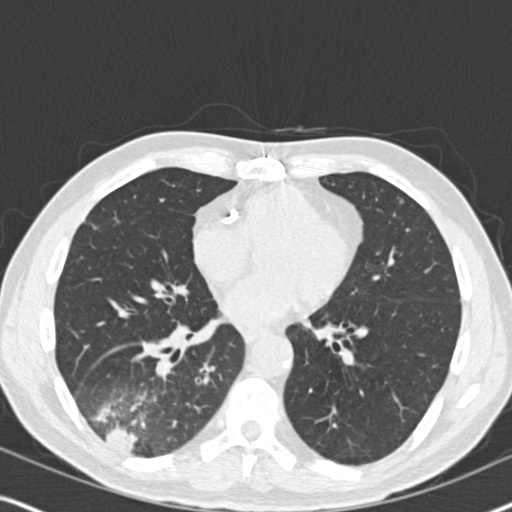
Low-dose screening chest CT, one axial slice; position 85 of 182 along the scan axis; reconstruction kernel B30f; lung window (W 1500 / L -600 HU); 2 mm slice thickness; 512 × 512 image matrix, field of view 330 × 330 mm.
Outlined on this slice (outlined manually by an expert reader):
- lesion 1 (tumor, lower lobe of right lung): box from (x=105, y=428) to (x=139, y=453) px